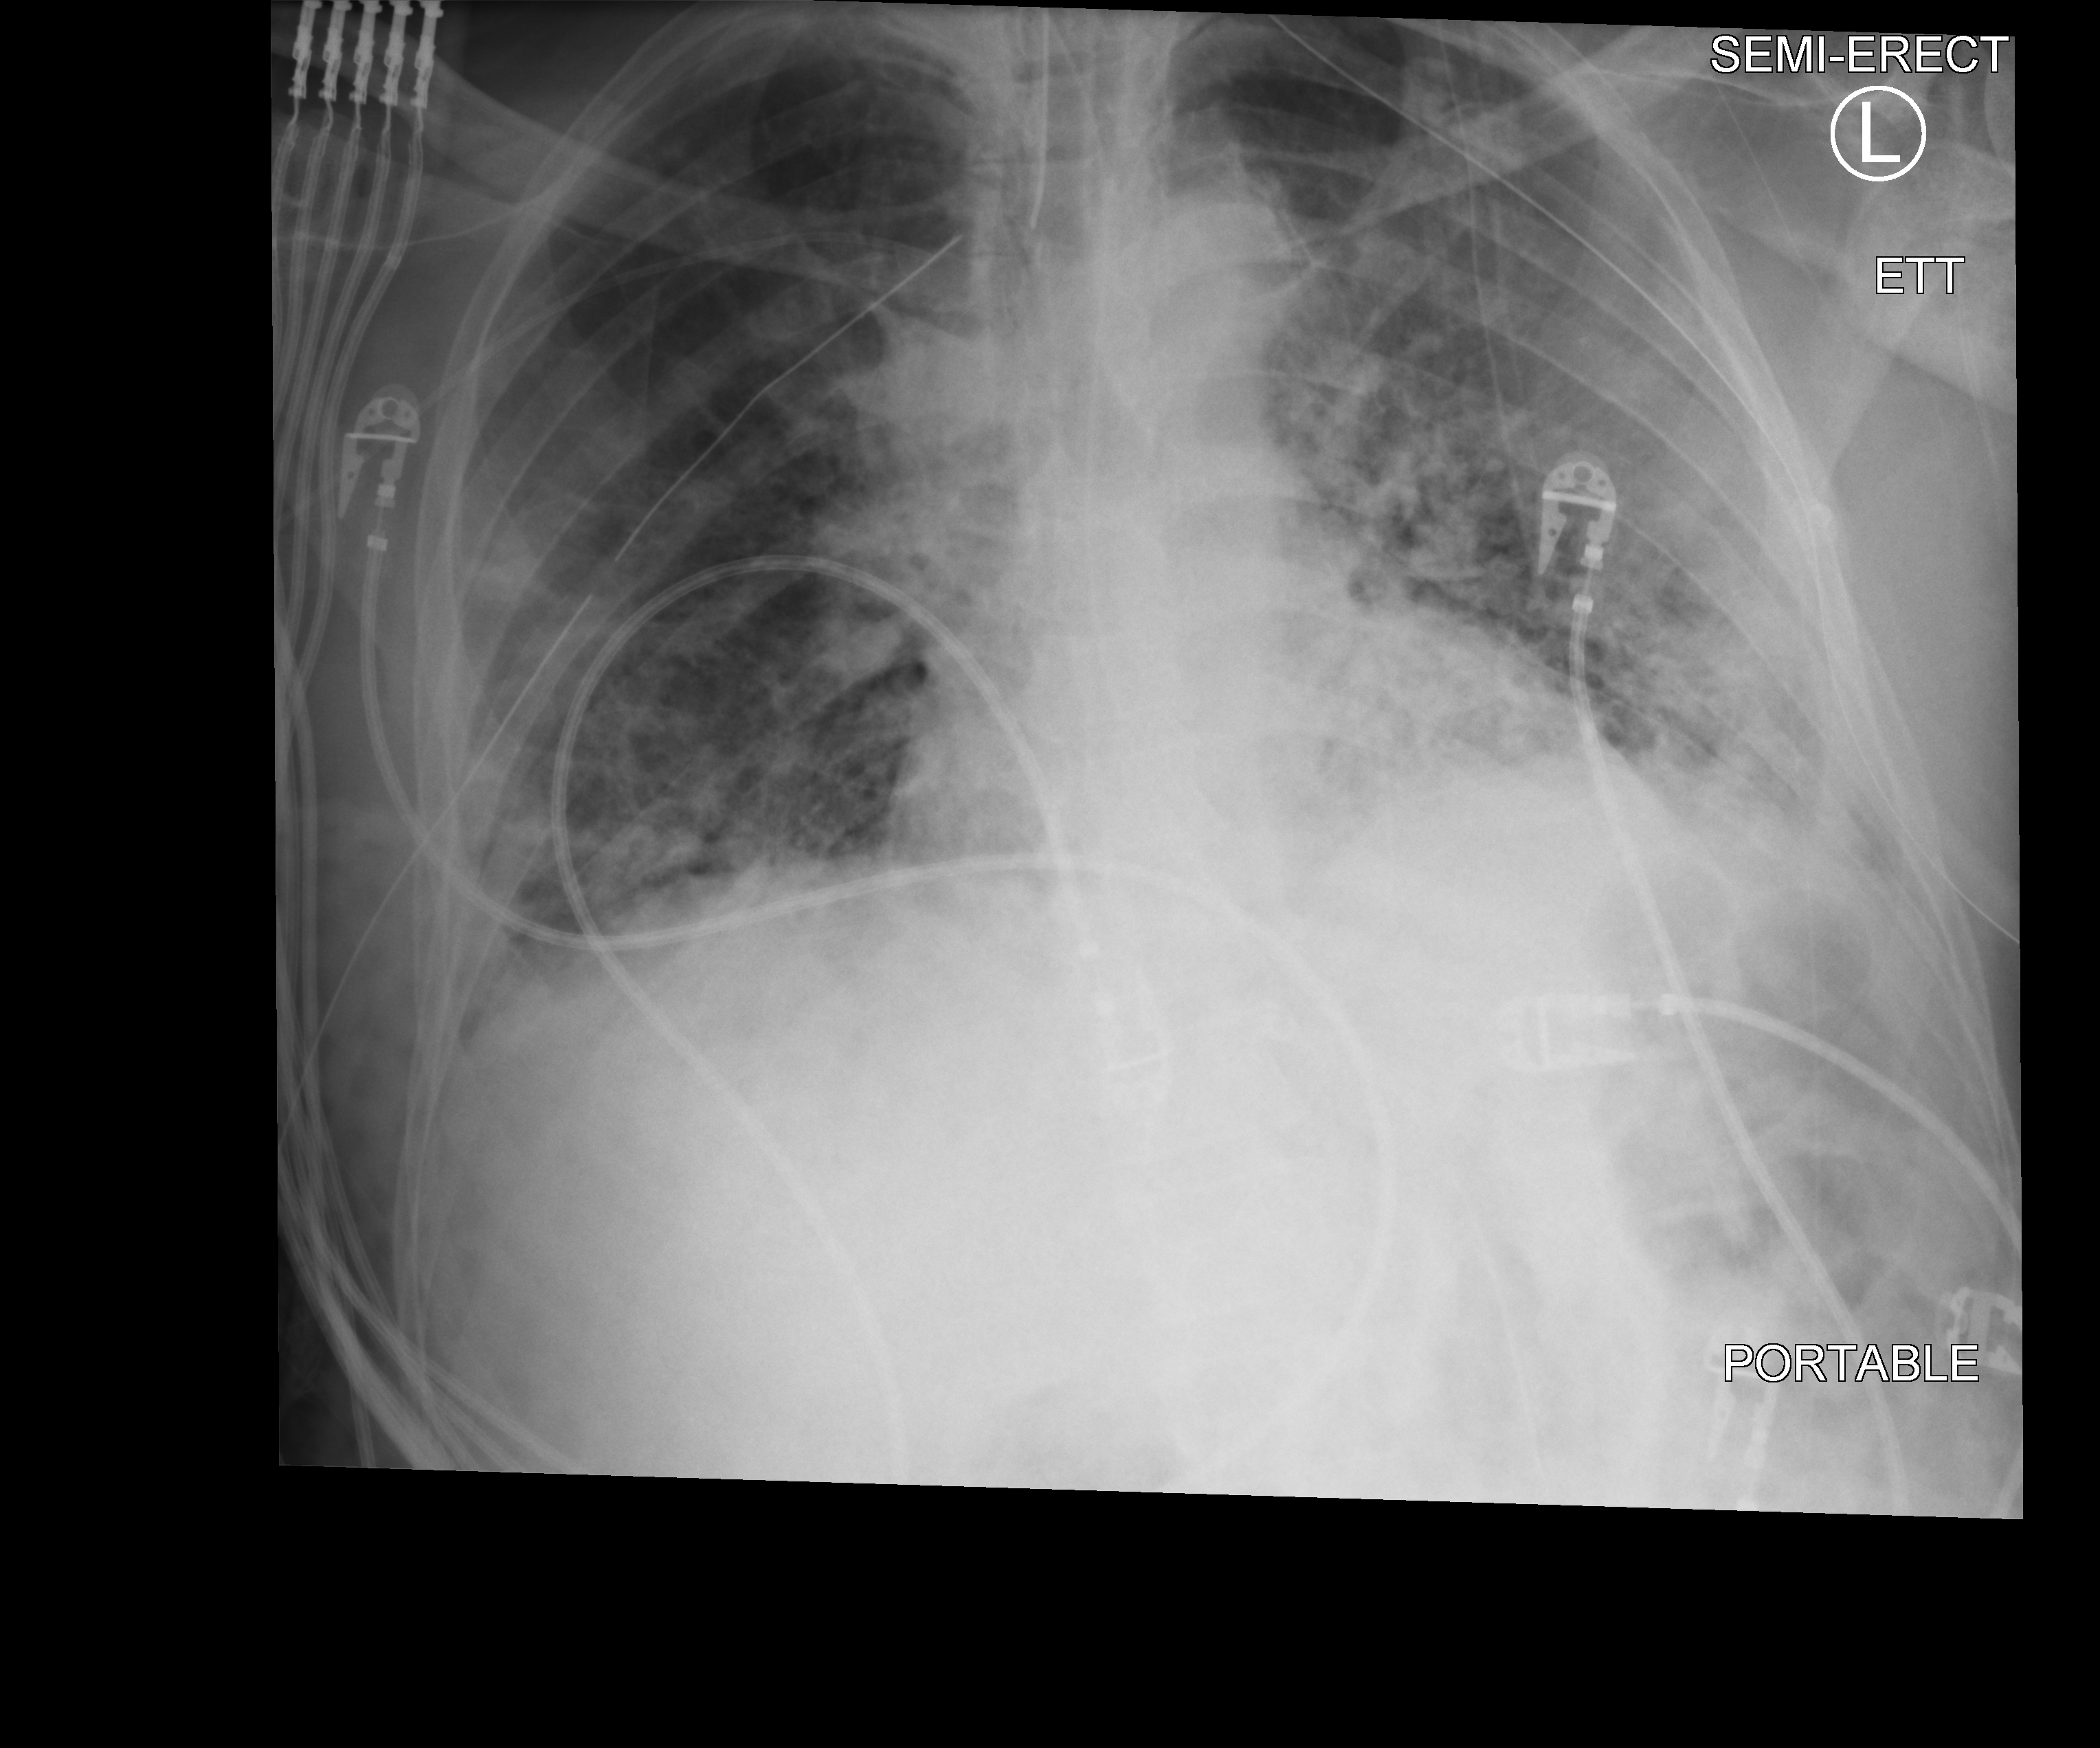
Portable chest radiograph; anteroposterior (AP) projection. Male patient hospitalised with COVID-19, age 18–59 years.
From the hospital-stay record, not from the radiograph (when in the stay this image was taken is not recorded):
- mechanically ventilated during this hospital stay: yes
- chronic kidney disease (admission record): no
- hypertension (admission record): no